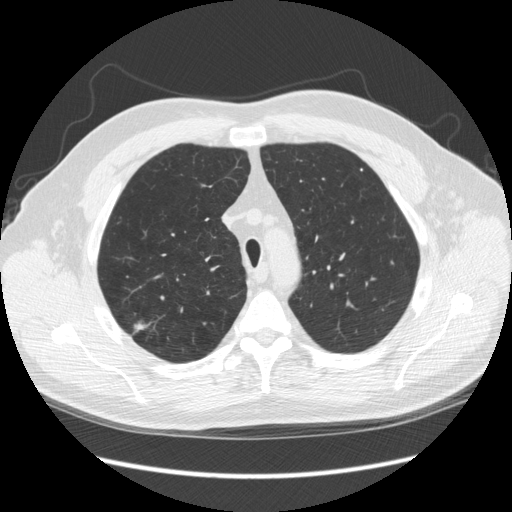
Low-dose screening chest CT, one axial slice; slice 193 of 248 in the series (ordered by position); reconstruction kernel STANDARD; 120 kVp; lung window (W 1500 / L -600 HU); 2.5 mm slice thickness; 512 × 512 image matrix.
Structures marked on this image (outlined manually by an expert reader):
- lesion 1 (tumor, upper lobe of right lung): box from (x=133, y=323) to (x=145, y=330) px